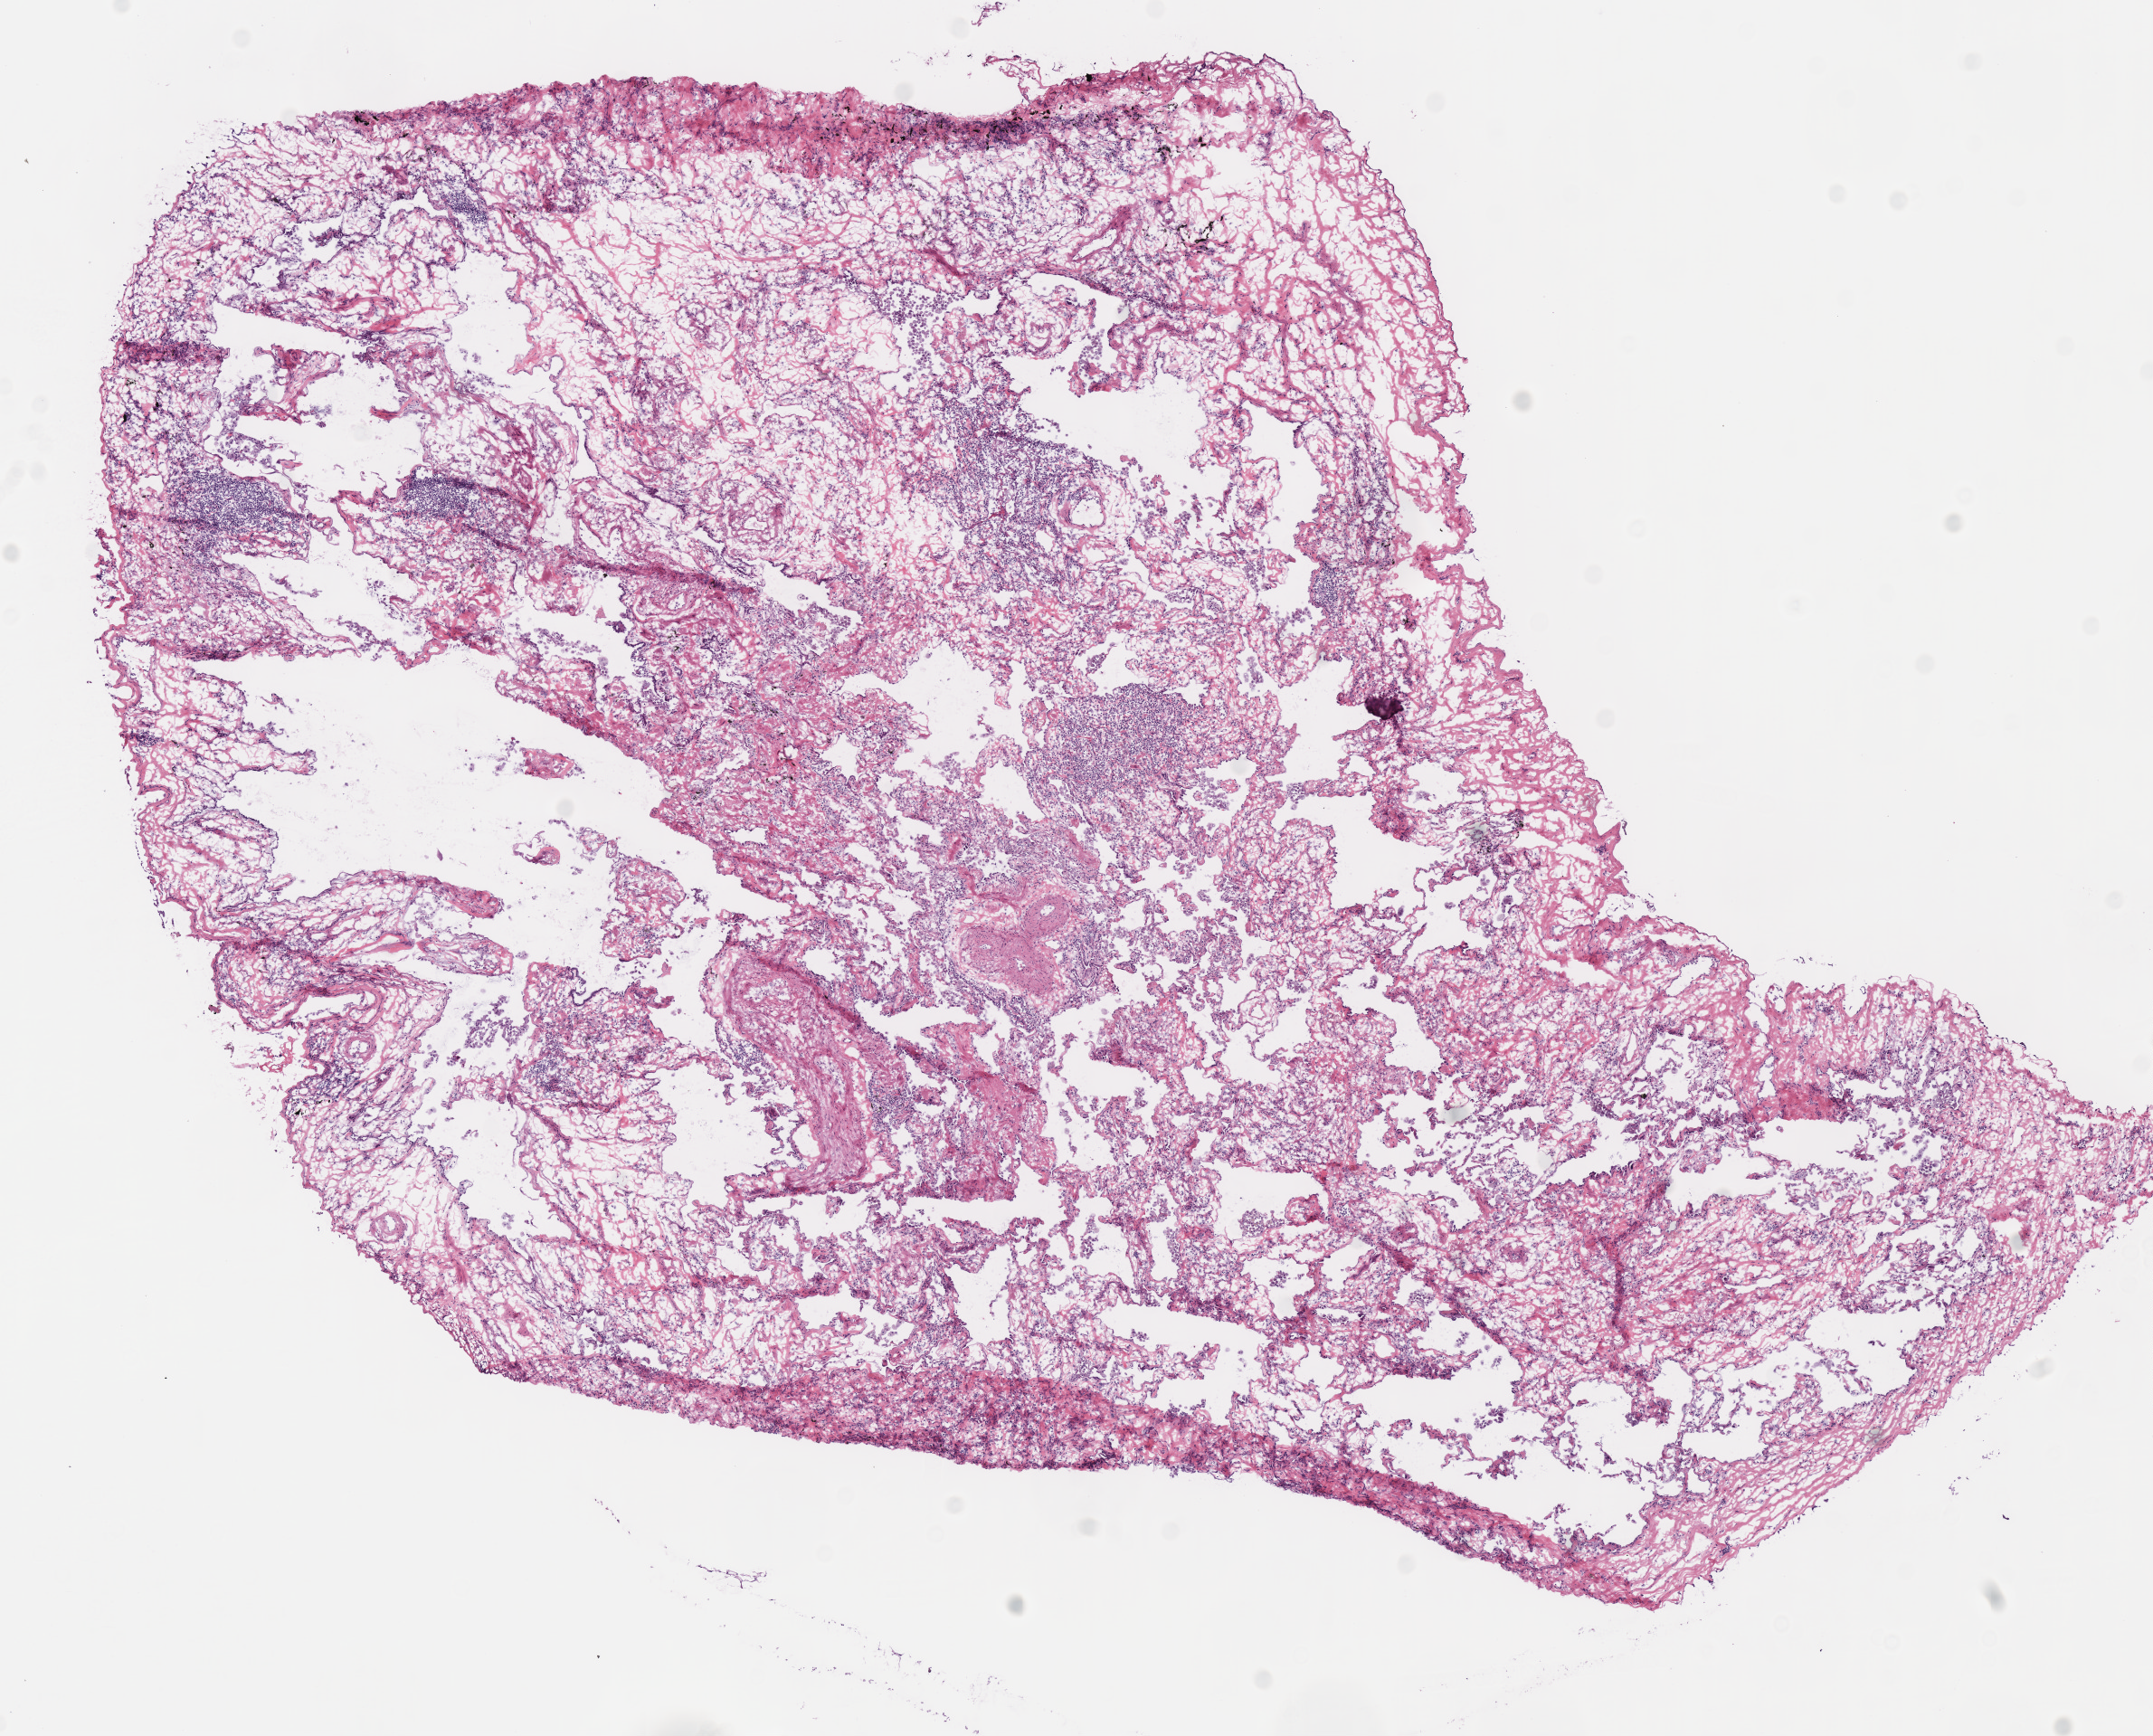
Digitized Hematoxylin and eosin (H&E) stained tissue section (whole slide), whole scanned area (about 9.4 x 7.6 mm, from a 40x scan) shown as a low-resolution overview. Frozen section. Sample: solid tissue normal (non-tumour tissue), lung. Patient: male, age at initial diagnosis 75 years.
This section: solid tissue normal (non-tumour) sample from the same patient. Patient diagnosis: Squamous cell carcinoma, NOS (upper lobe, lung).